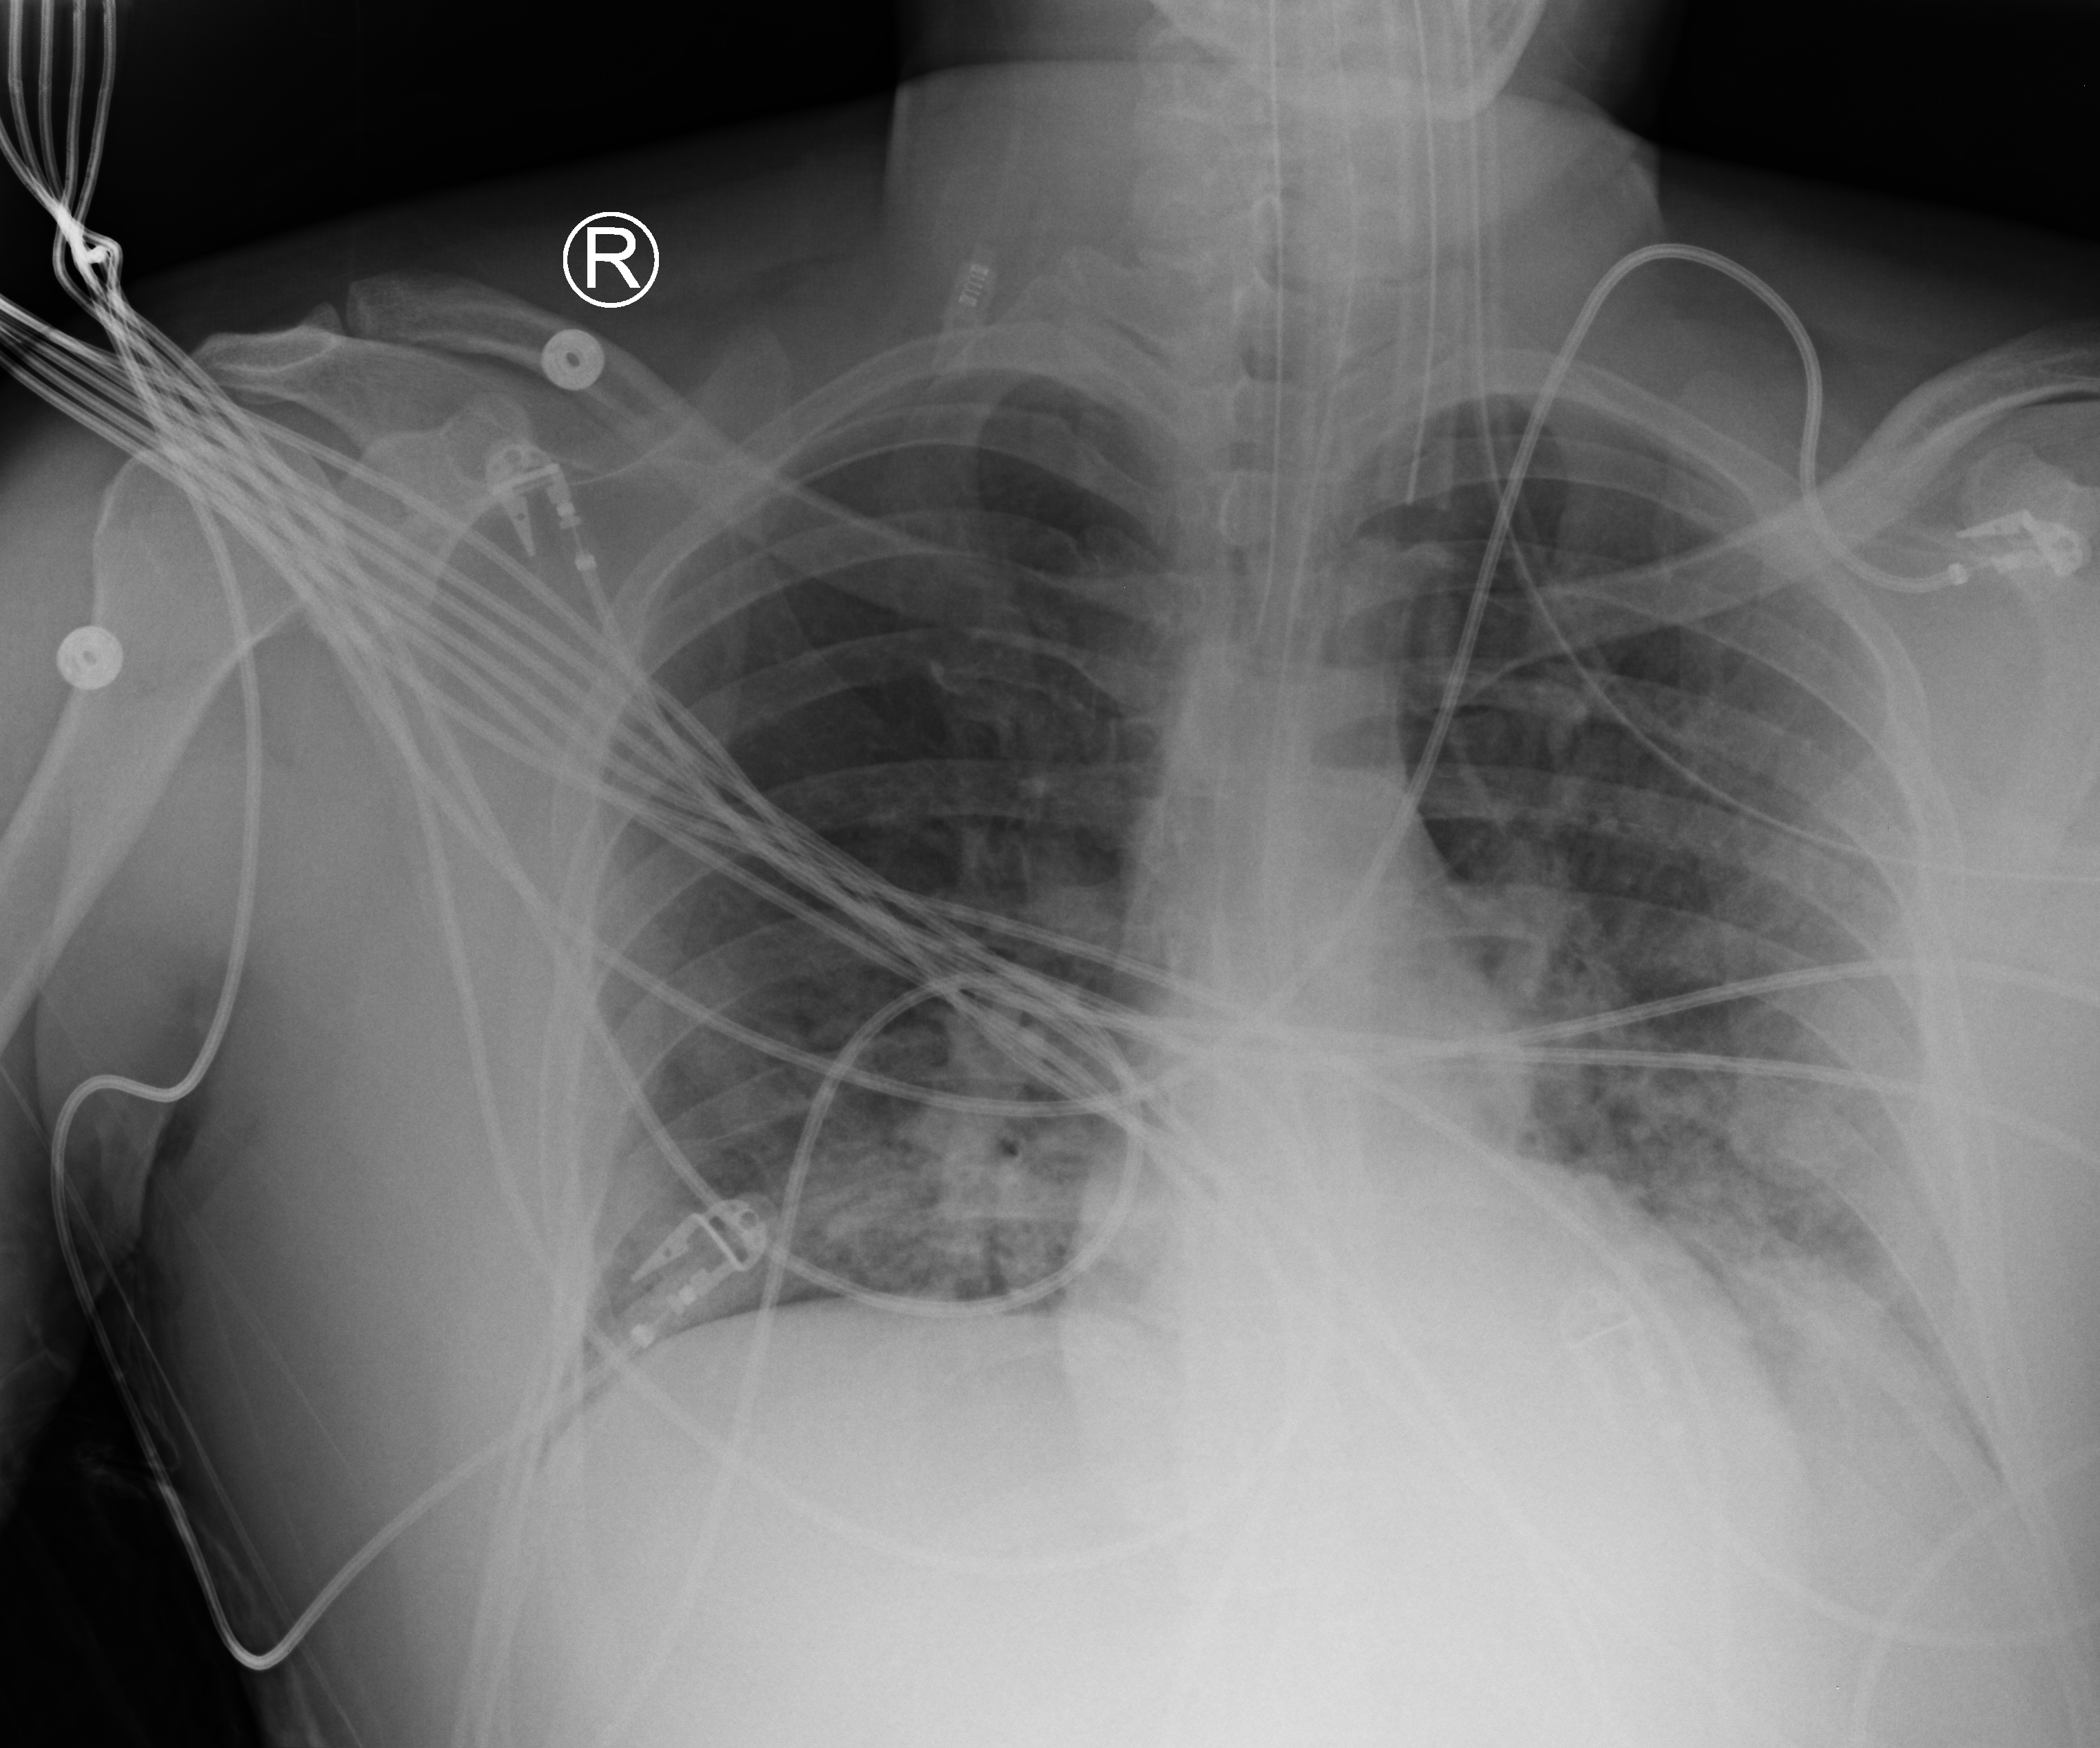
Bedside chest radiograph (computed radiography); anteroposterior (AP) projection. Male patient hospitalised with COVID-19, age 18–59 years.
Hospital-stay facts (about this admission, not read from this image; timing relative to this image not recorded): mechanically ventilated during this hospital stay: yes; length of hospital stay: 22 days.